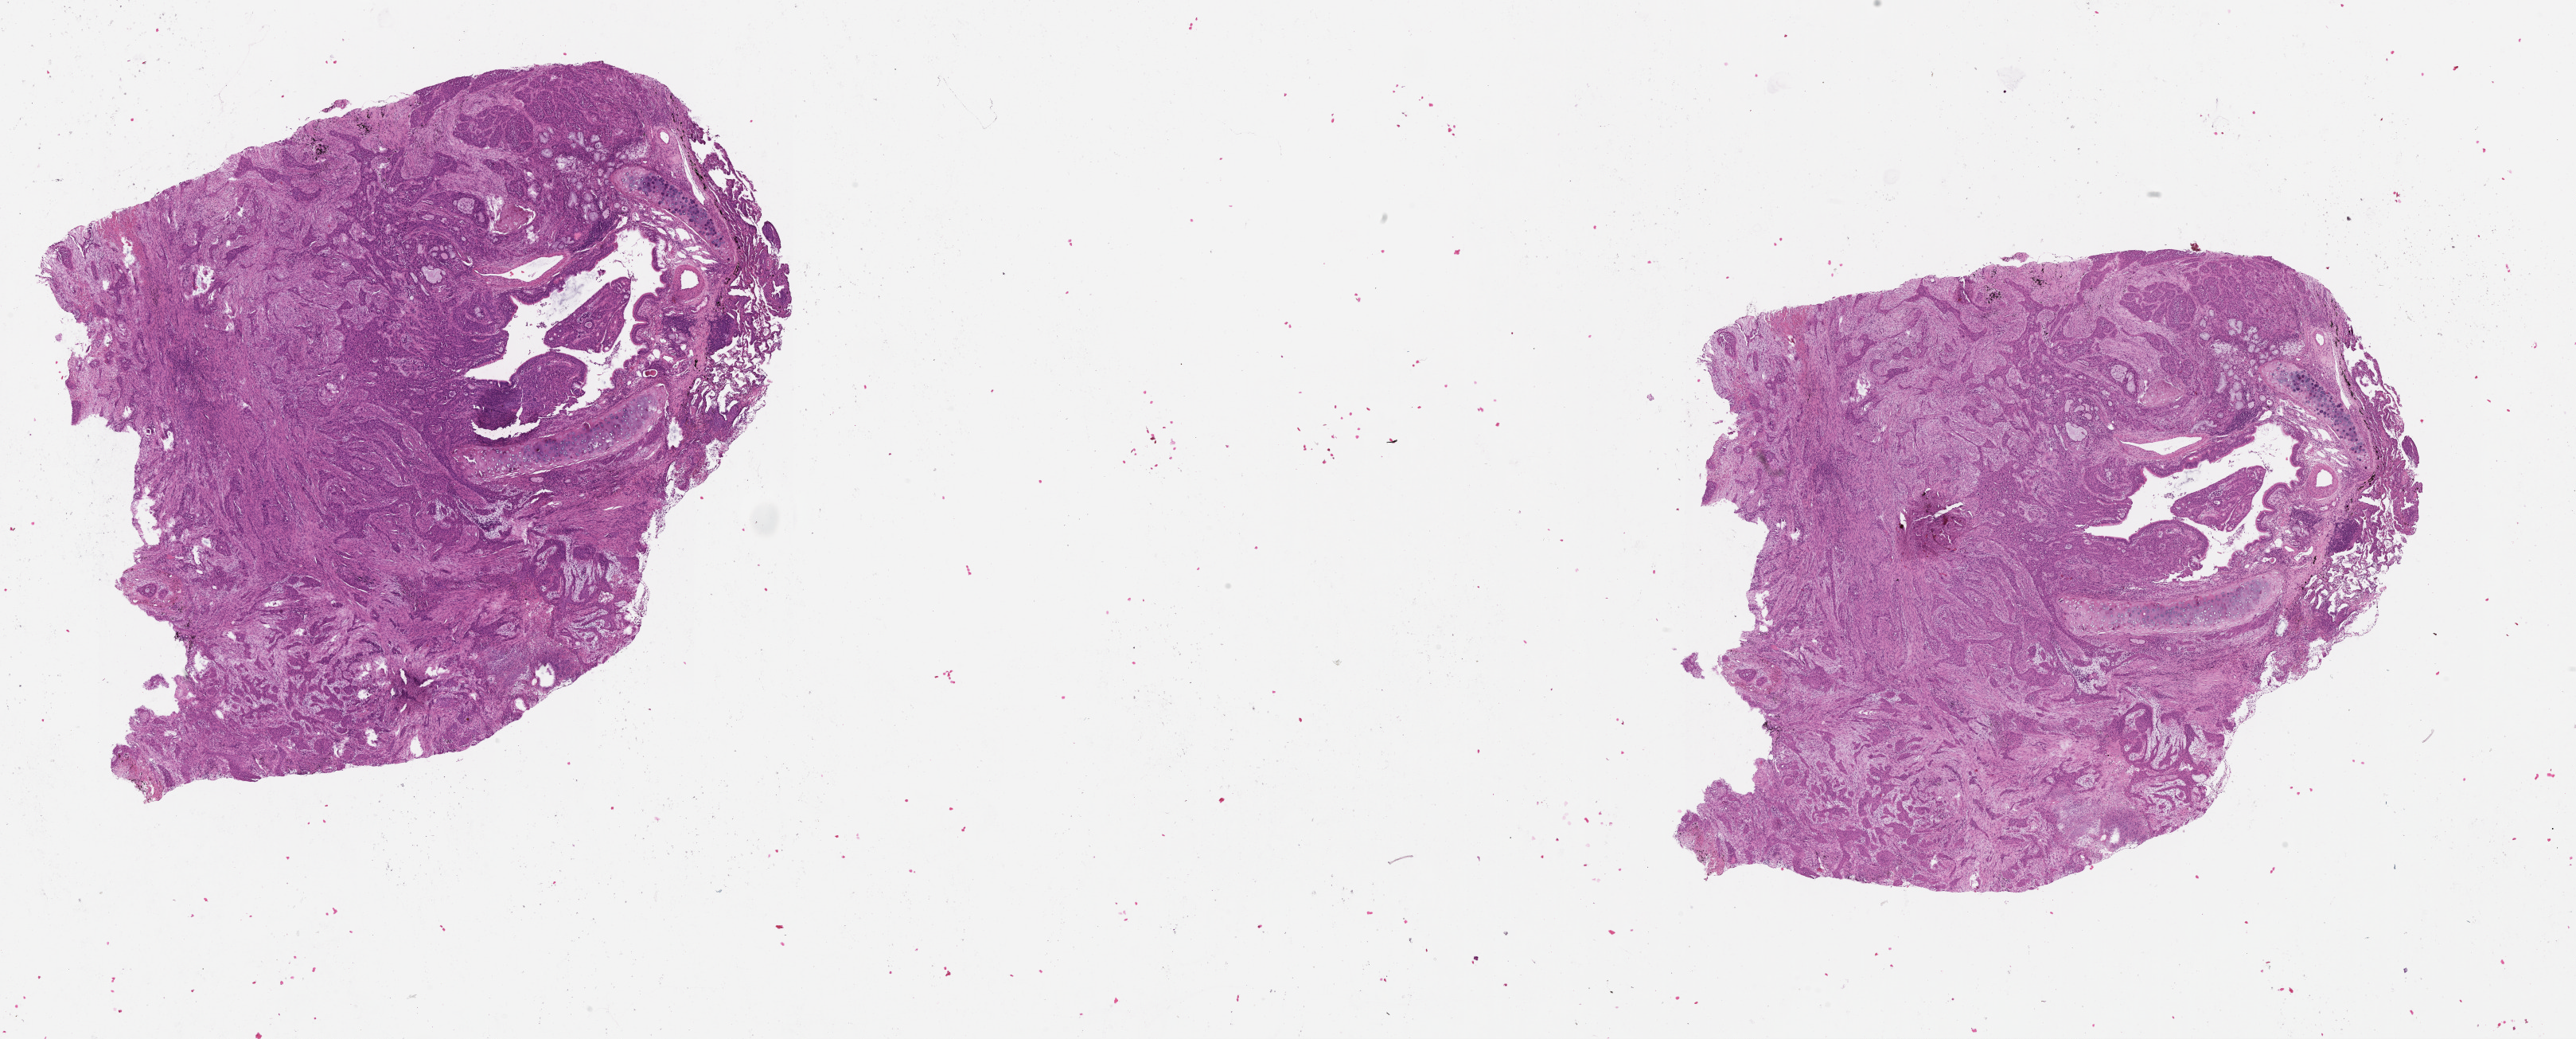
Whole-slide histology image, H&E-stained, whole scanned area (about 26.1 x 10.5 mm) shown as a low-resolution overview. Tumour tissue sample, lung. 79-year-old male patient.
• patient diagnosis (cohort enrolment): squamous cell carcinoma (lung)